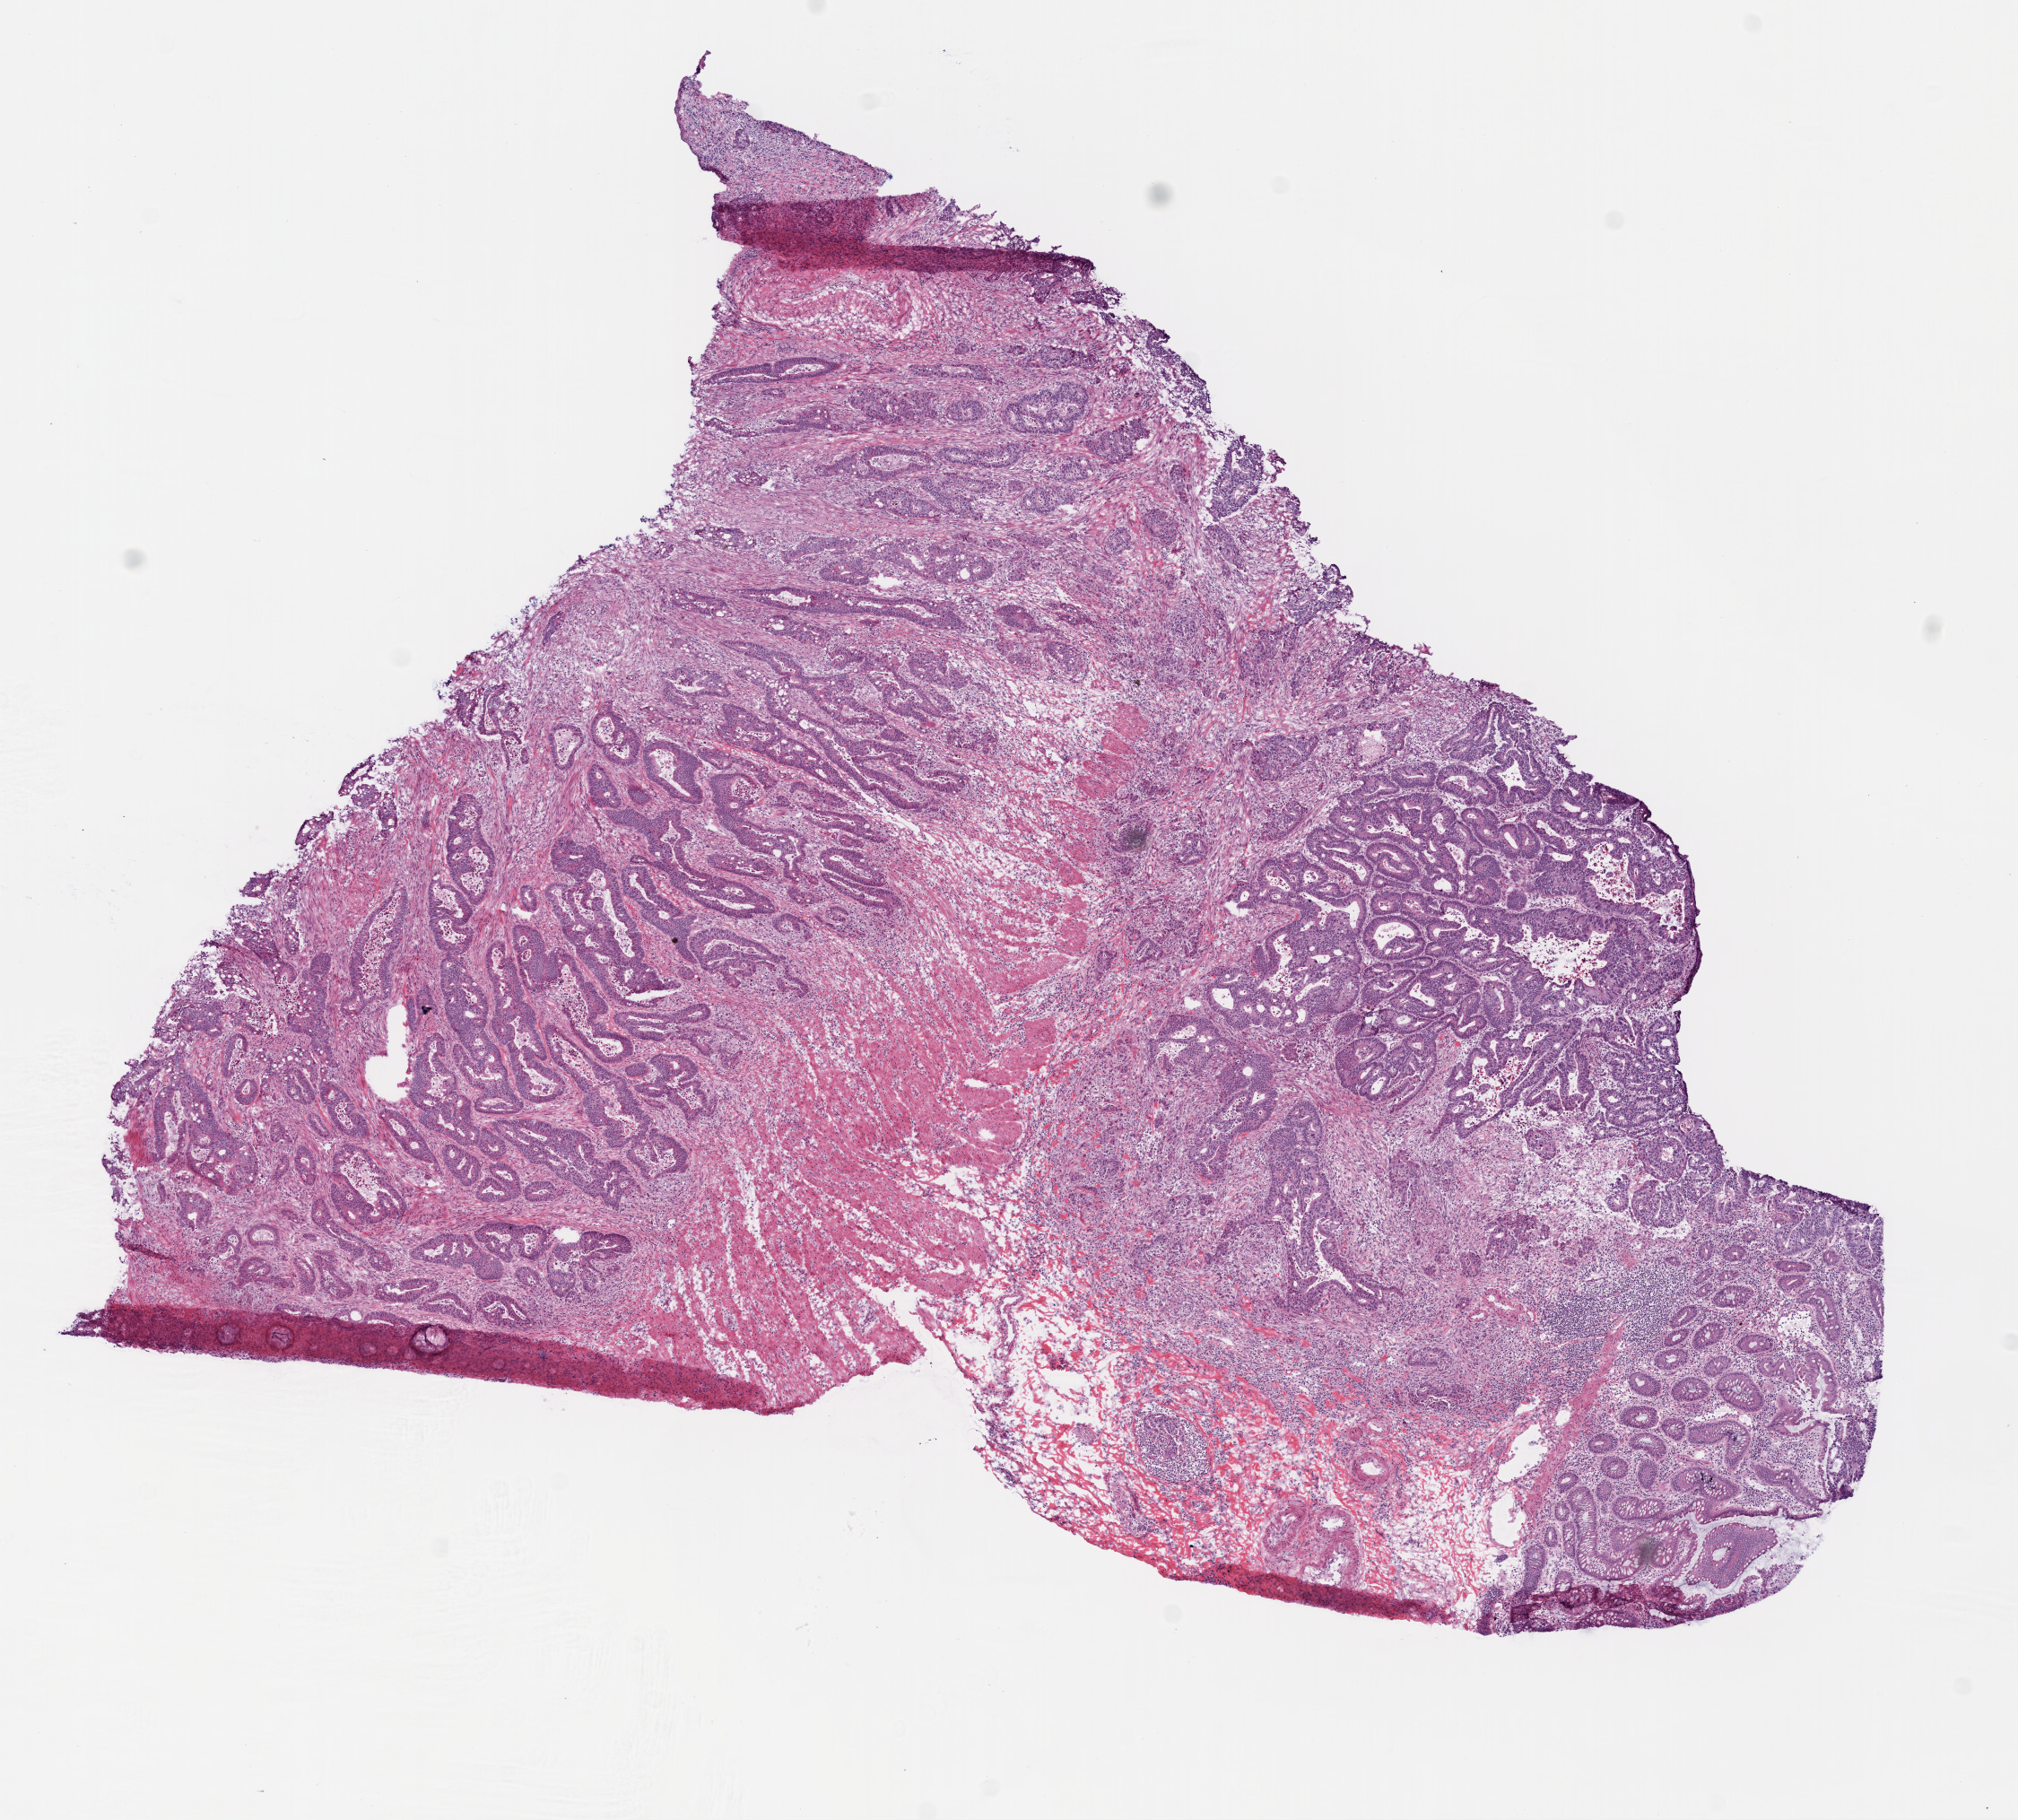
Digitized H&E tissue section (whole slide), shown as a low-resolution overview of the whole scanned area (about 9.0 x 8.1 mm, from a 20x scan). Frozen section. Sample: primary tumour, colon. Female patient; age at initial diagnosis 85 years. Pathologist review of this section (percent, as recorded): tumour cells 66%, tumour nuclei 70%, normal cells 8%, stromal cells 18%, necrosis 8%.
• lymph nodes positive (case pathology): 0 of 23 examined
• diagnosis: Adenocarcinoma with mixed subtypes
• AJCC pathologic stage: IIA
• TNM: T3 N0 M0